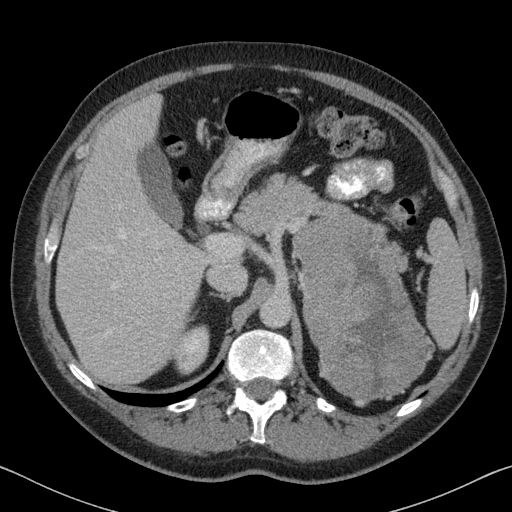
Contrast-enhanced abdominal CT, one axial slice; slice 52 of 88 in the series (ordered by position); reconstruction kernel B31f; 120 kVp; intravenous contrast given; soft-tissue window (W 400 / L 40 HU); 3 mm slice thickness; 512 × 512 image matrix, field of view 366 × 366 mm. Male patient, age 51 years. From the clinical record (not read from this slice): diagnosis: adrenocortical carcinoma; tumour side: left adrenal; tumour size at pathology: 16.5 cm; Ki-67 index: 30 %; stage (as recorded): 2.
Structures marked on this image (semi-automatically segmented with operator editing):
- mass: box from (x=293, y=208) to (x=434, y=400) px